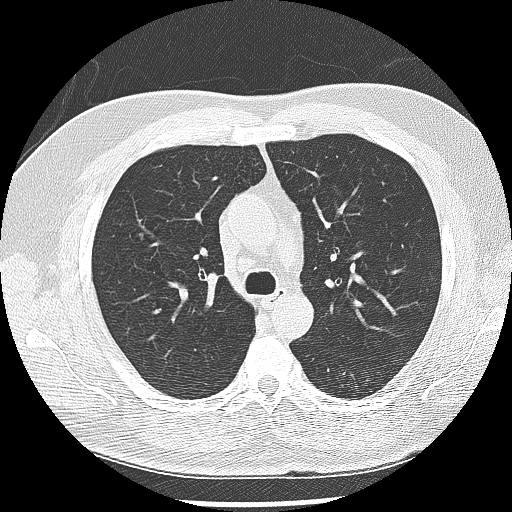
Low-dose screening chest CT, one axial slice; position 181 of 265 along the scan axis; lung window (W 1500 / L -600 HU); 2.5 mm slice thickness; 512 × 512 image matrix.
Annotated regions visible in this slice (outlined manually by an expert reader):
- lesion 1 (tumor, upper lobe of right lung): bounding box <139,233,143,240> (left, top, right, bottom; pixels)